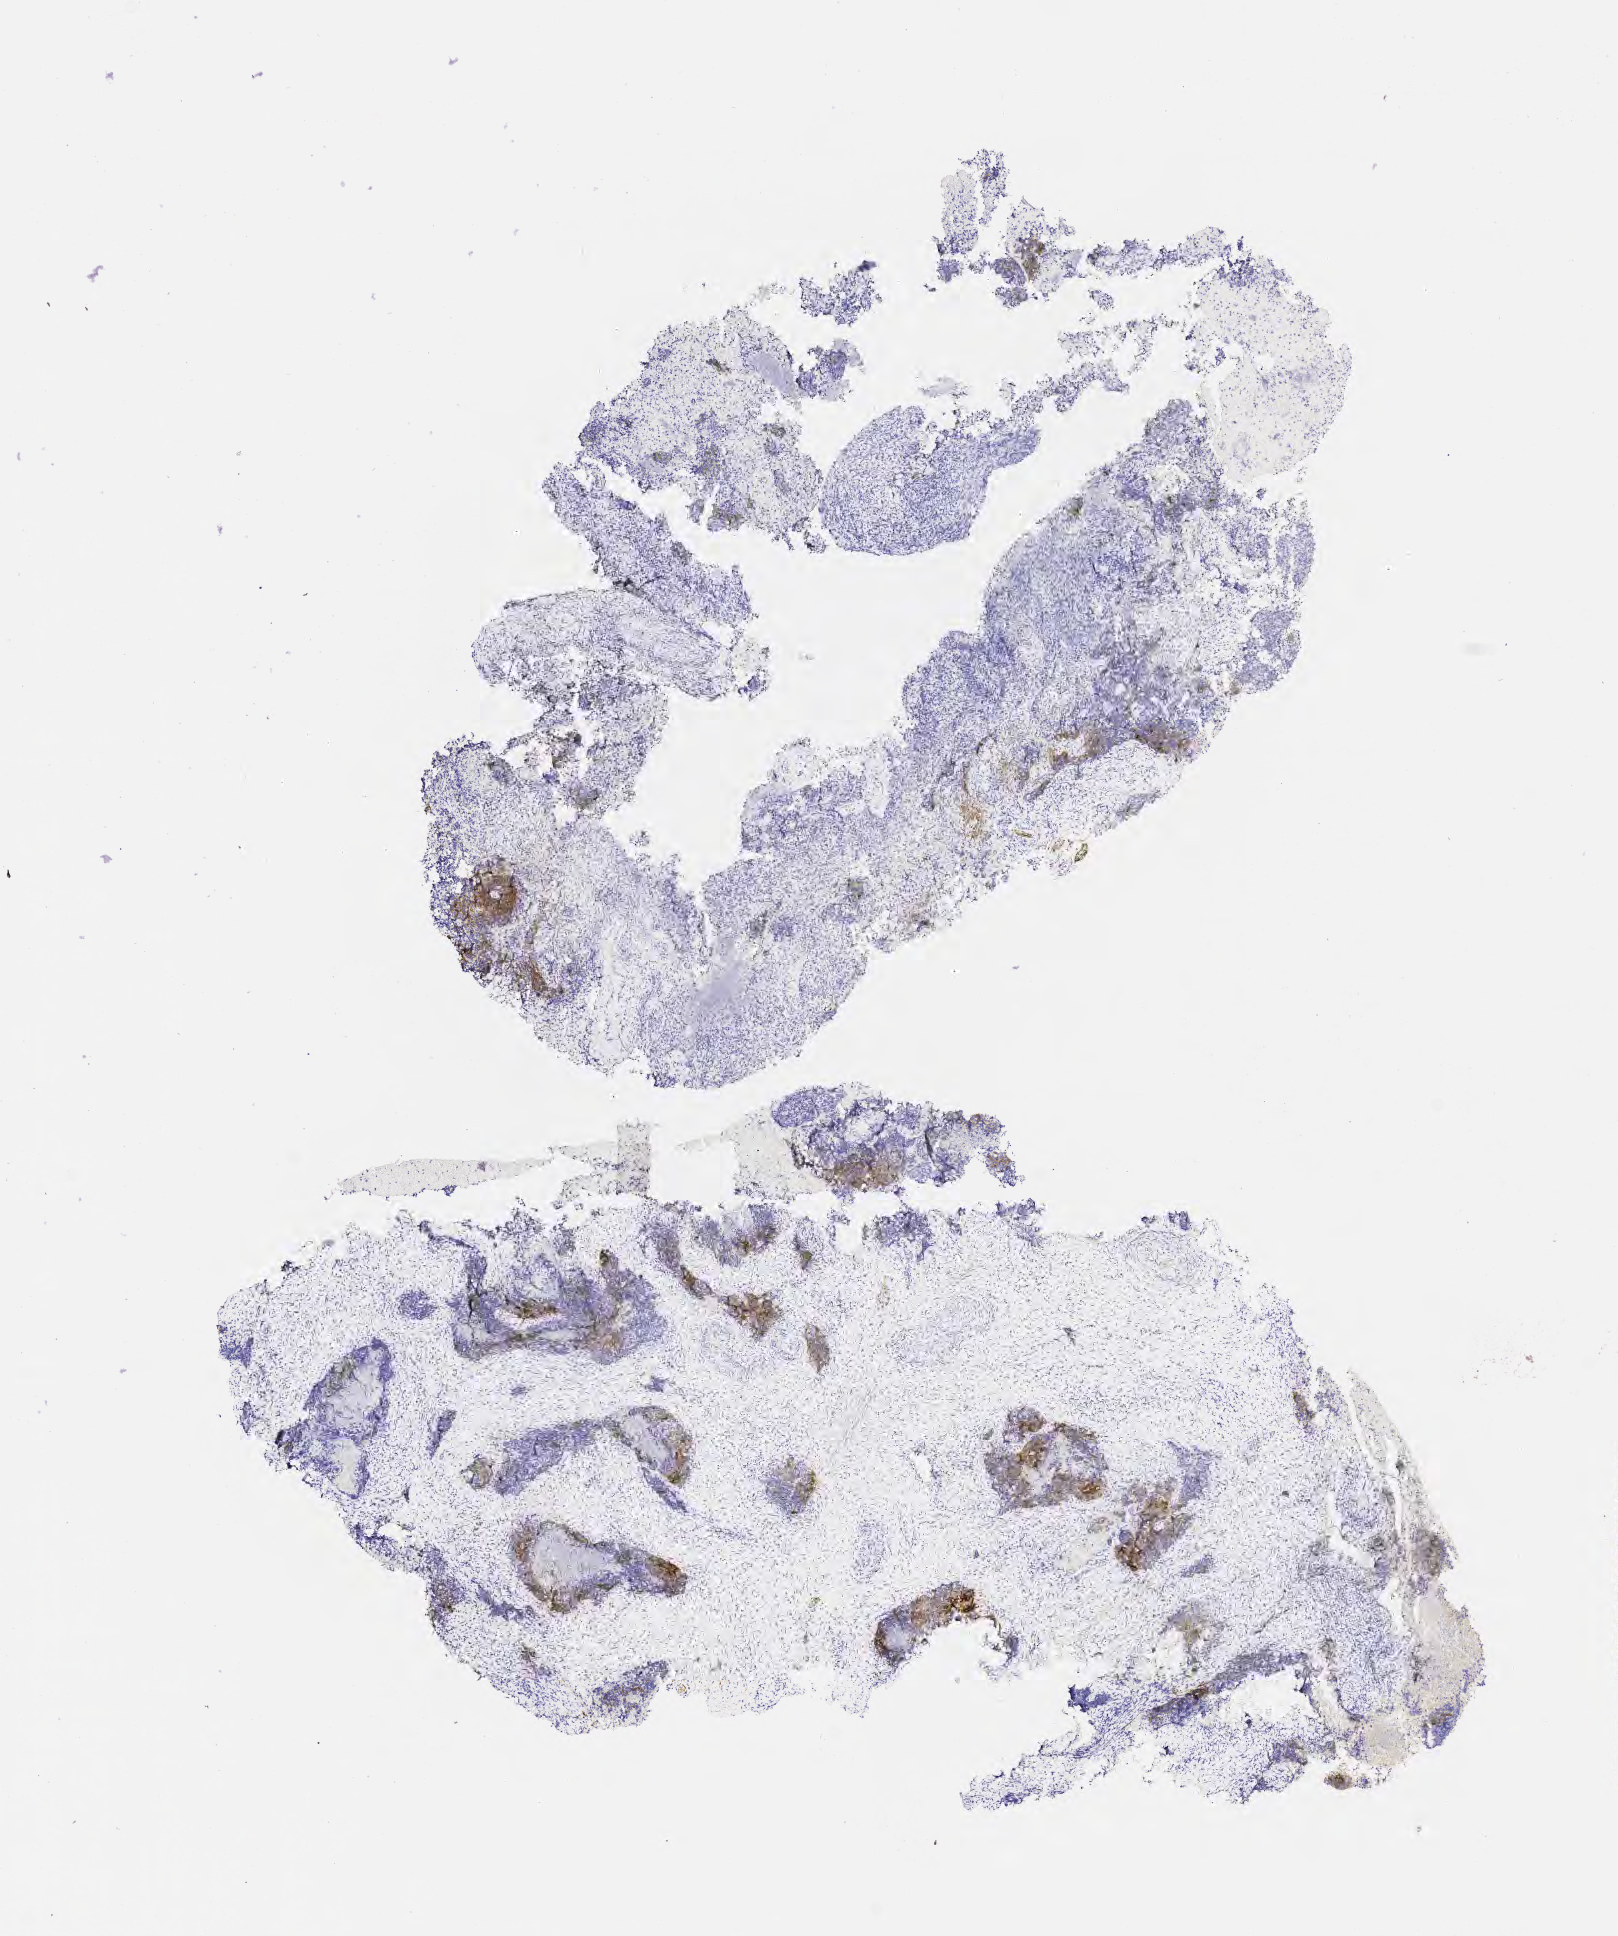
Whole-slide image, immunohistochemical stain for CD56, whole scanned area (about 6.5 x 7.8 mm) shown as a low-resolution overview, tumor tissue, site: cervix. Female patient, 47 years old.
Diagnosis: Squamous cell carcinoma, large cell, nonkeratinizing, NOS.